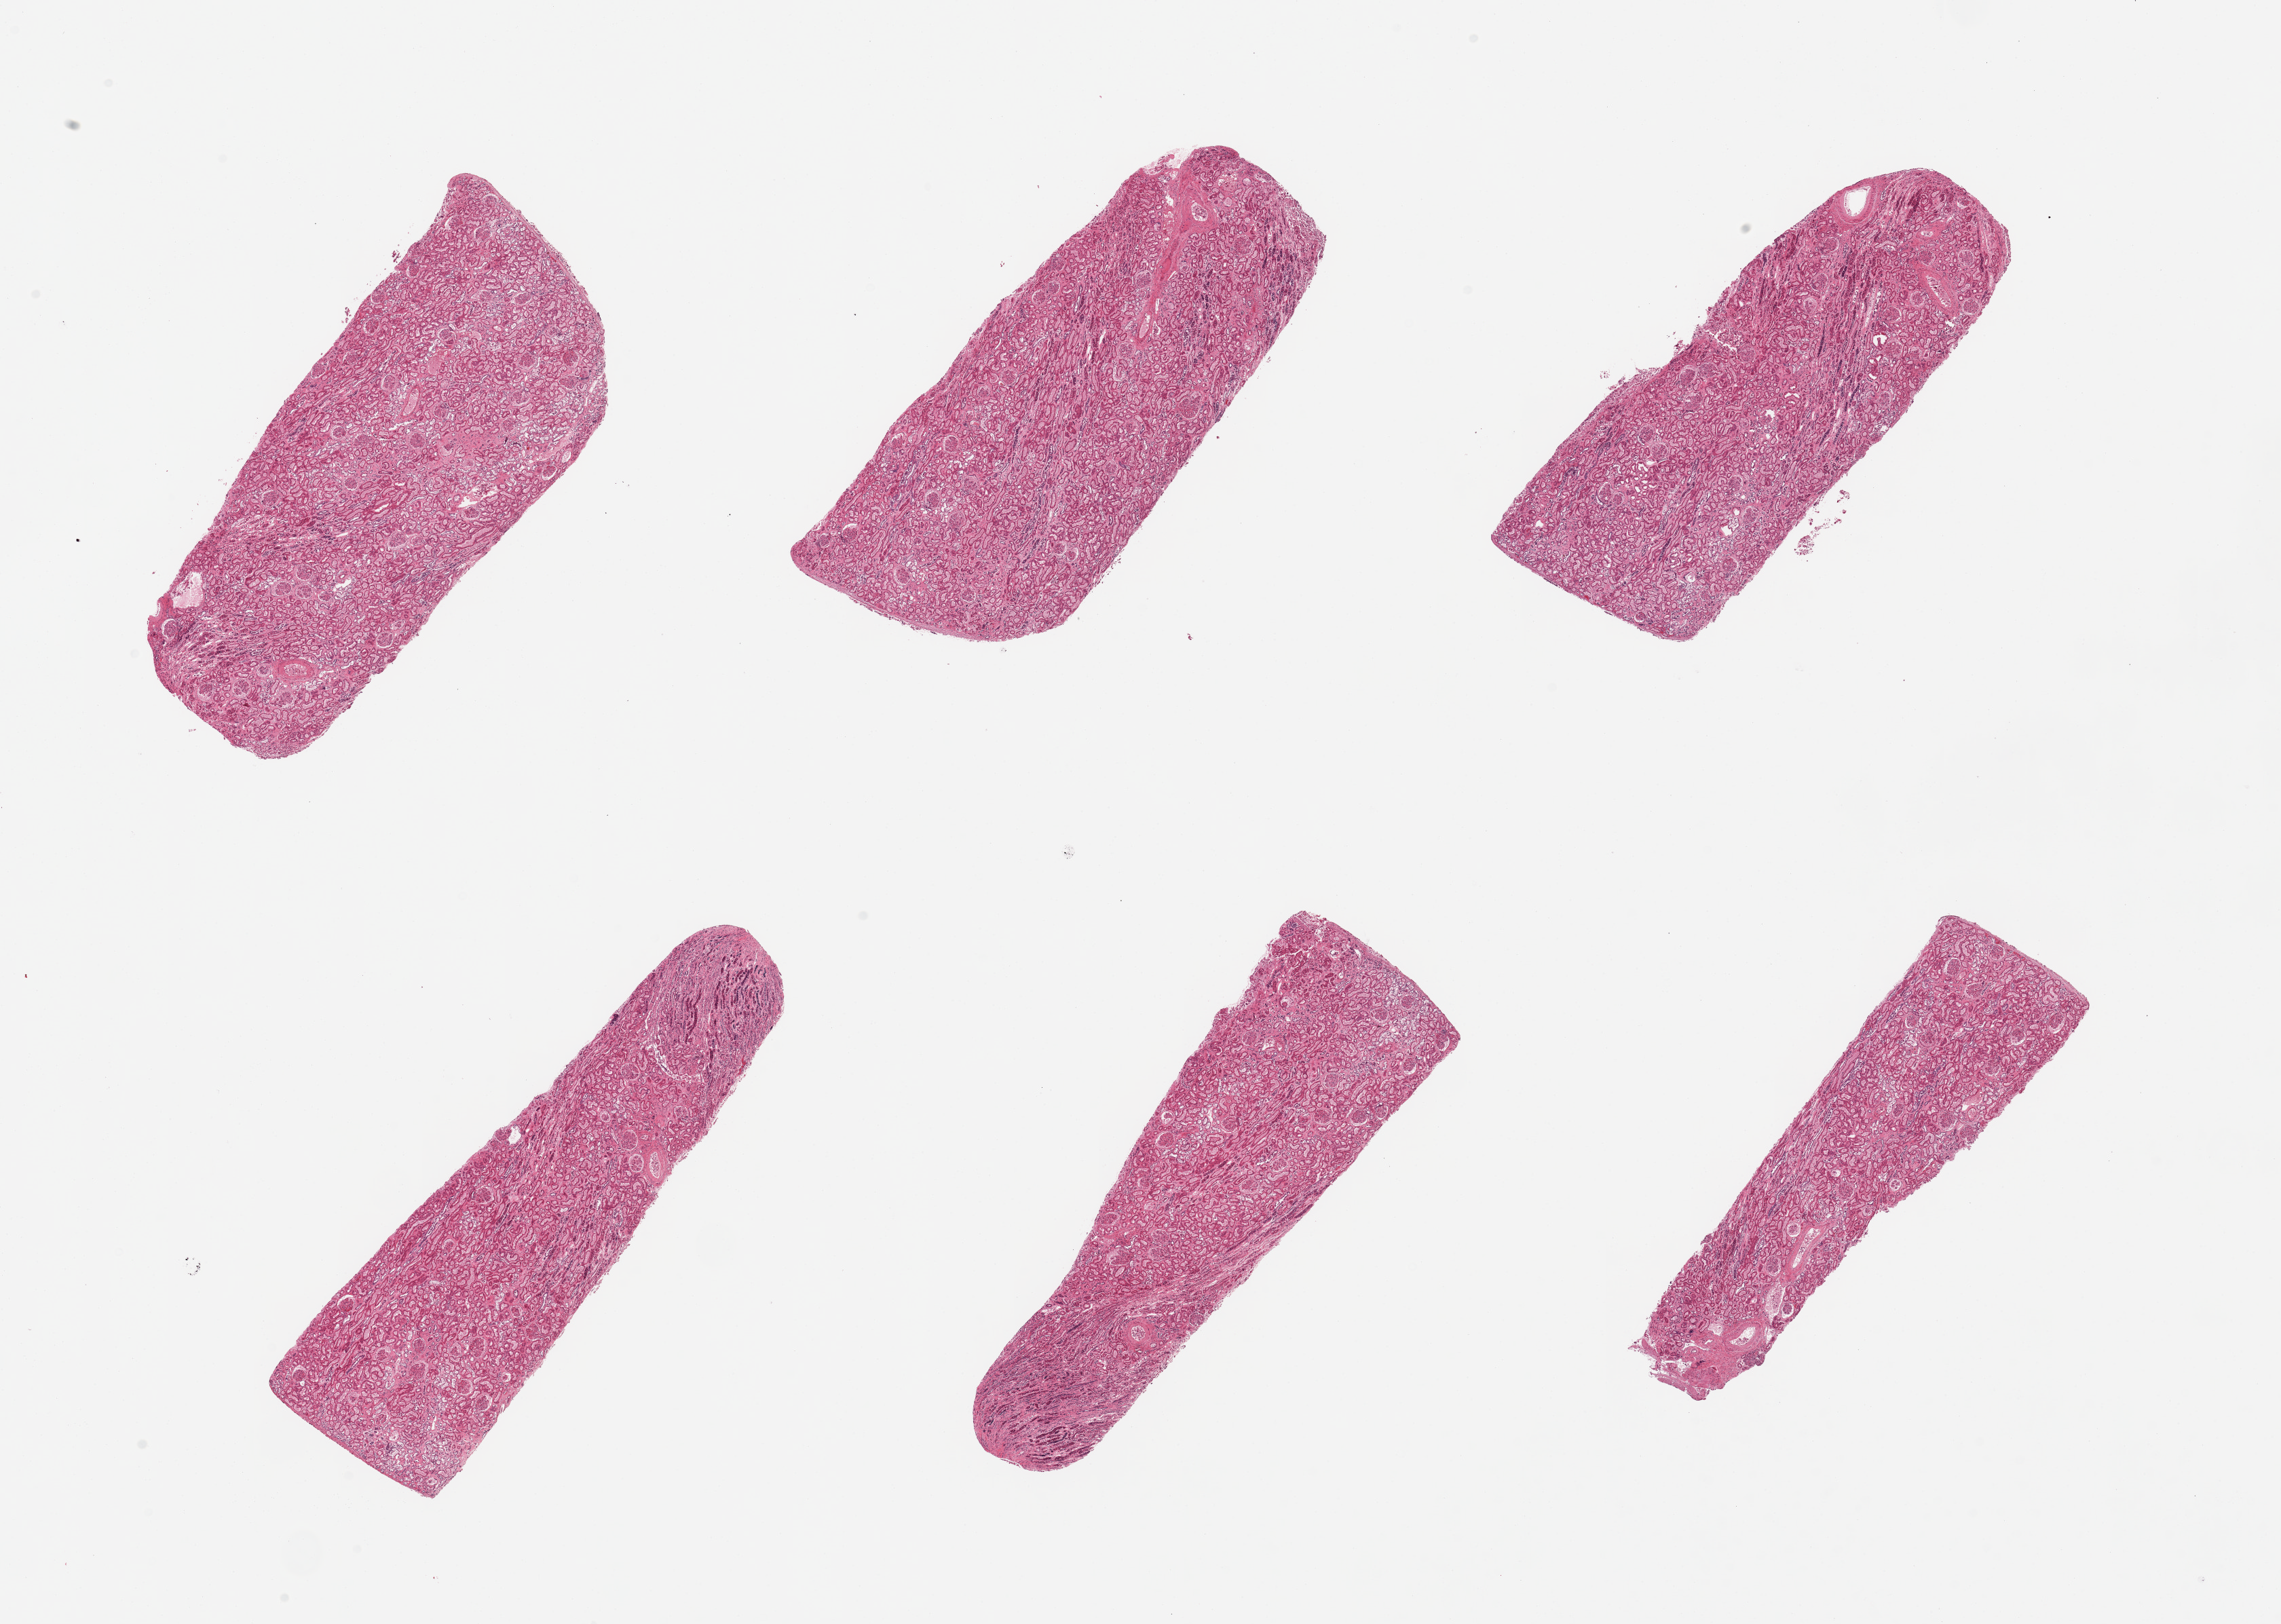
Digitized hematoxylin and eosin (H&E)-stained section, brightfield — low-resolution overview of the scanned area, about 26.6 x 18.9 mm. PAXgene-fixed paraffin-embedded (PFPE) section. Section of renal cortex (target tissue). Donor tissue sample. Donor sex: male.
Review note (as recorded): 6 pieces; no sign of chronic or active disease.